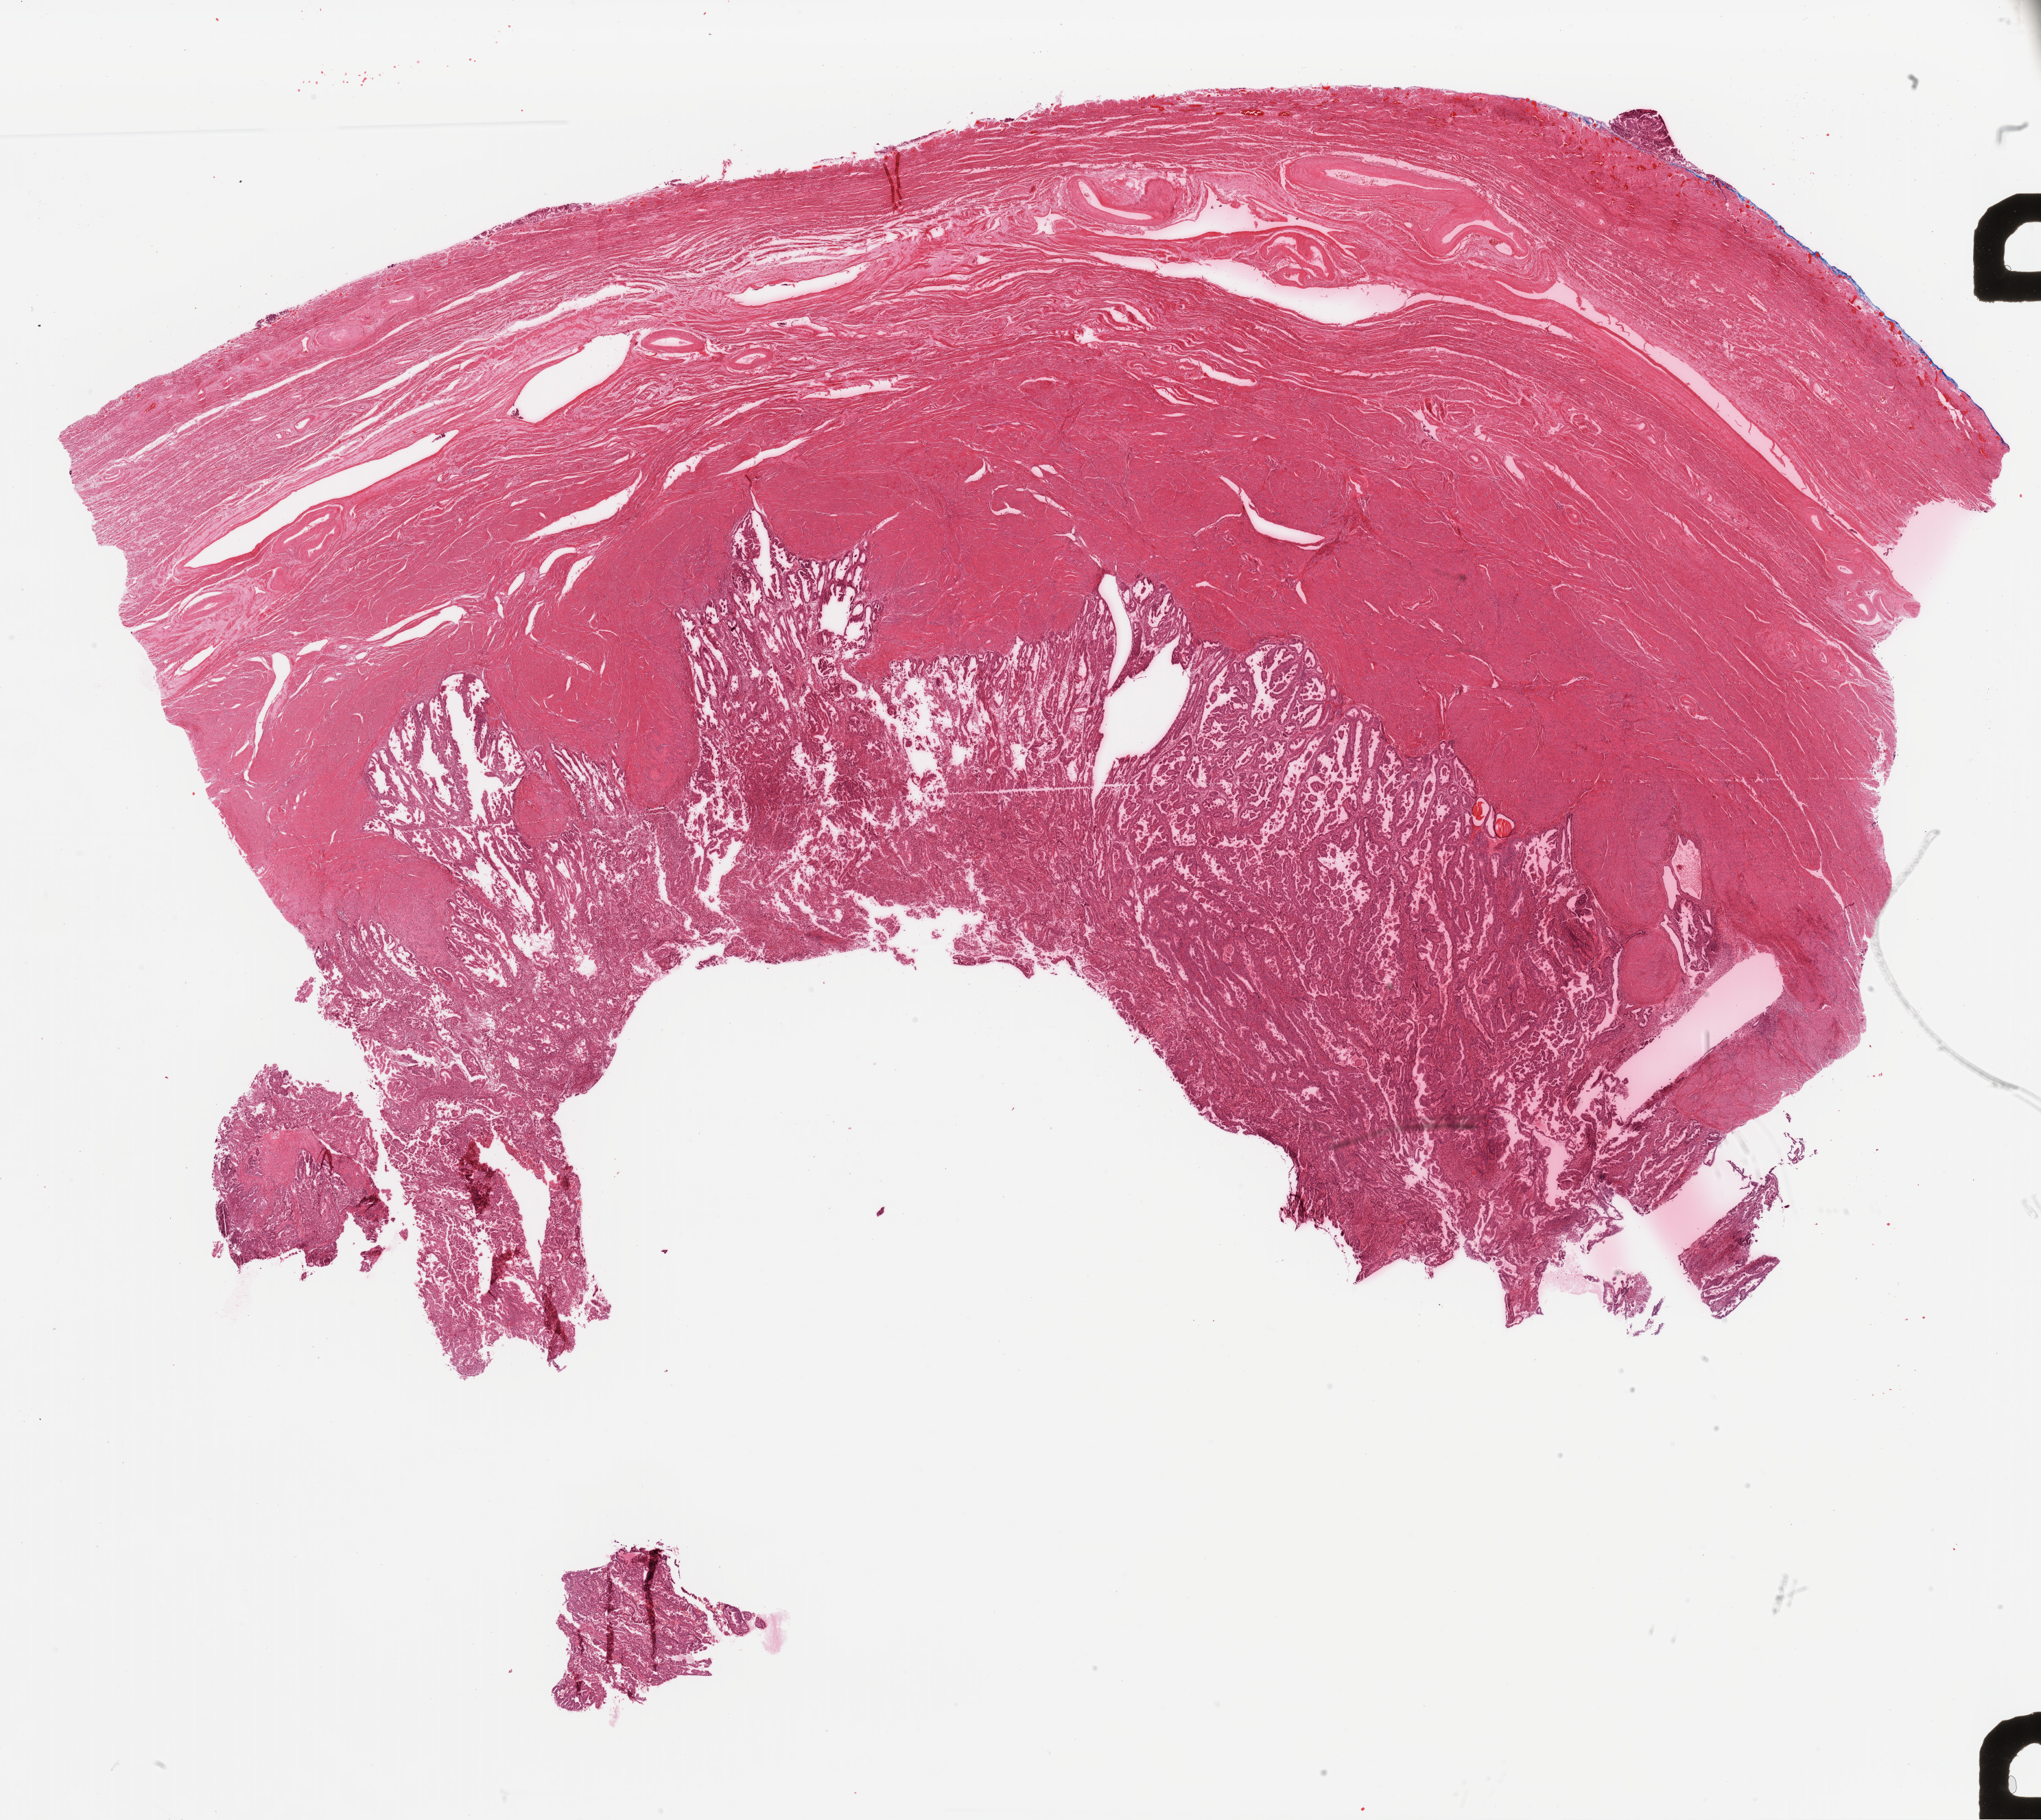
Hematoxylin and eosin (H&E) stained whole-slide image — a low-resolution overview of the entire scanned area, about 23.5 x 21.0 mm (slide scanned at 40x). Formalin-fixed paraffin-embedded (FFPE) diagnostic section. Uterus, primary tumour sample. Female patient; age at initial diagnosis 79 years.
Histologic diagnosis: Serous cystadenocarcinoma, NOS (endometrium).